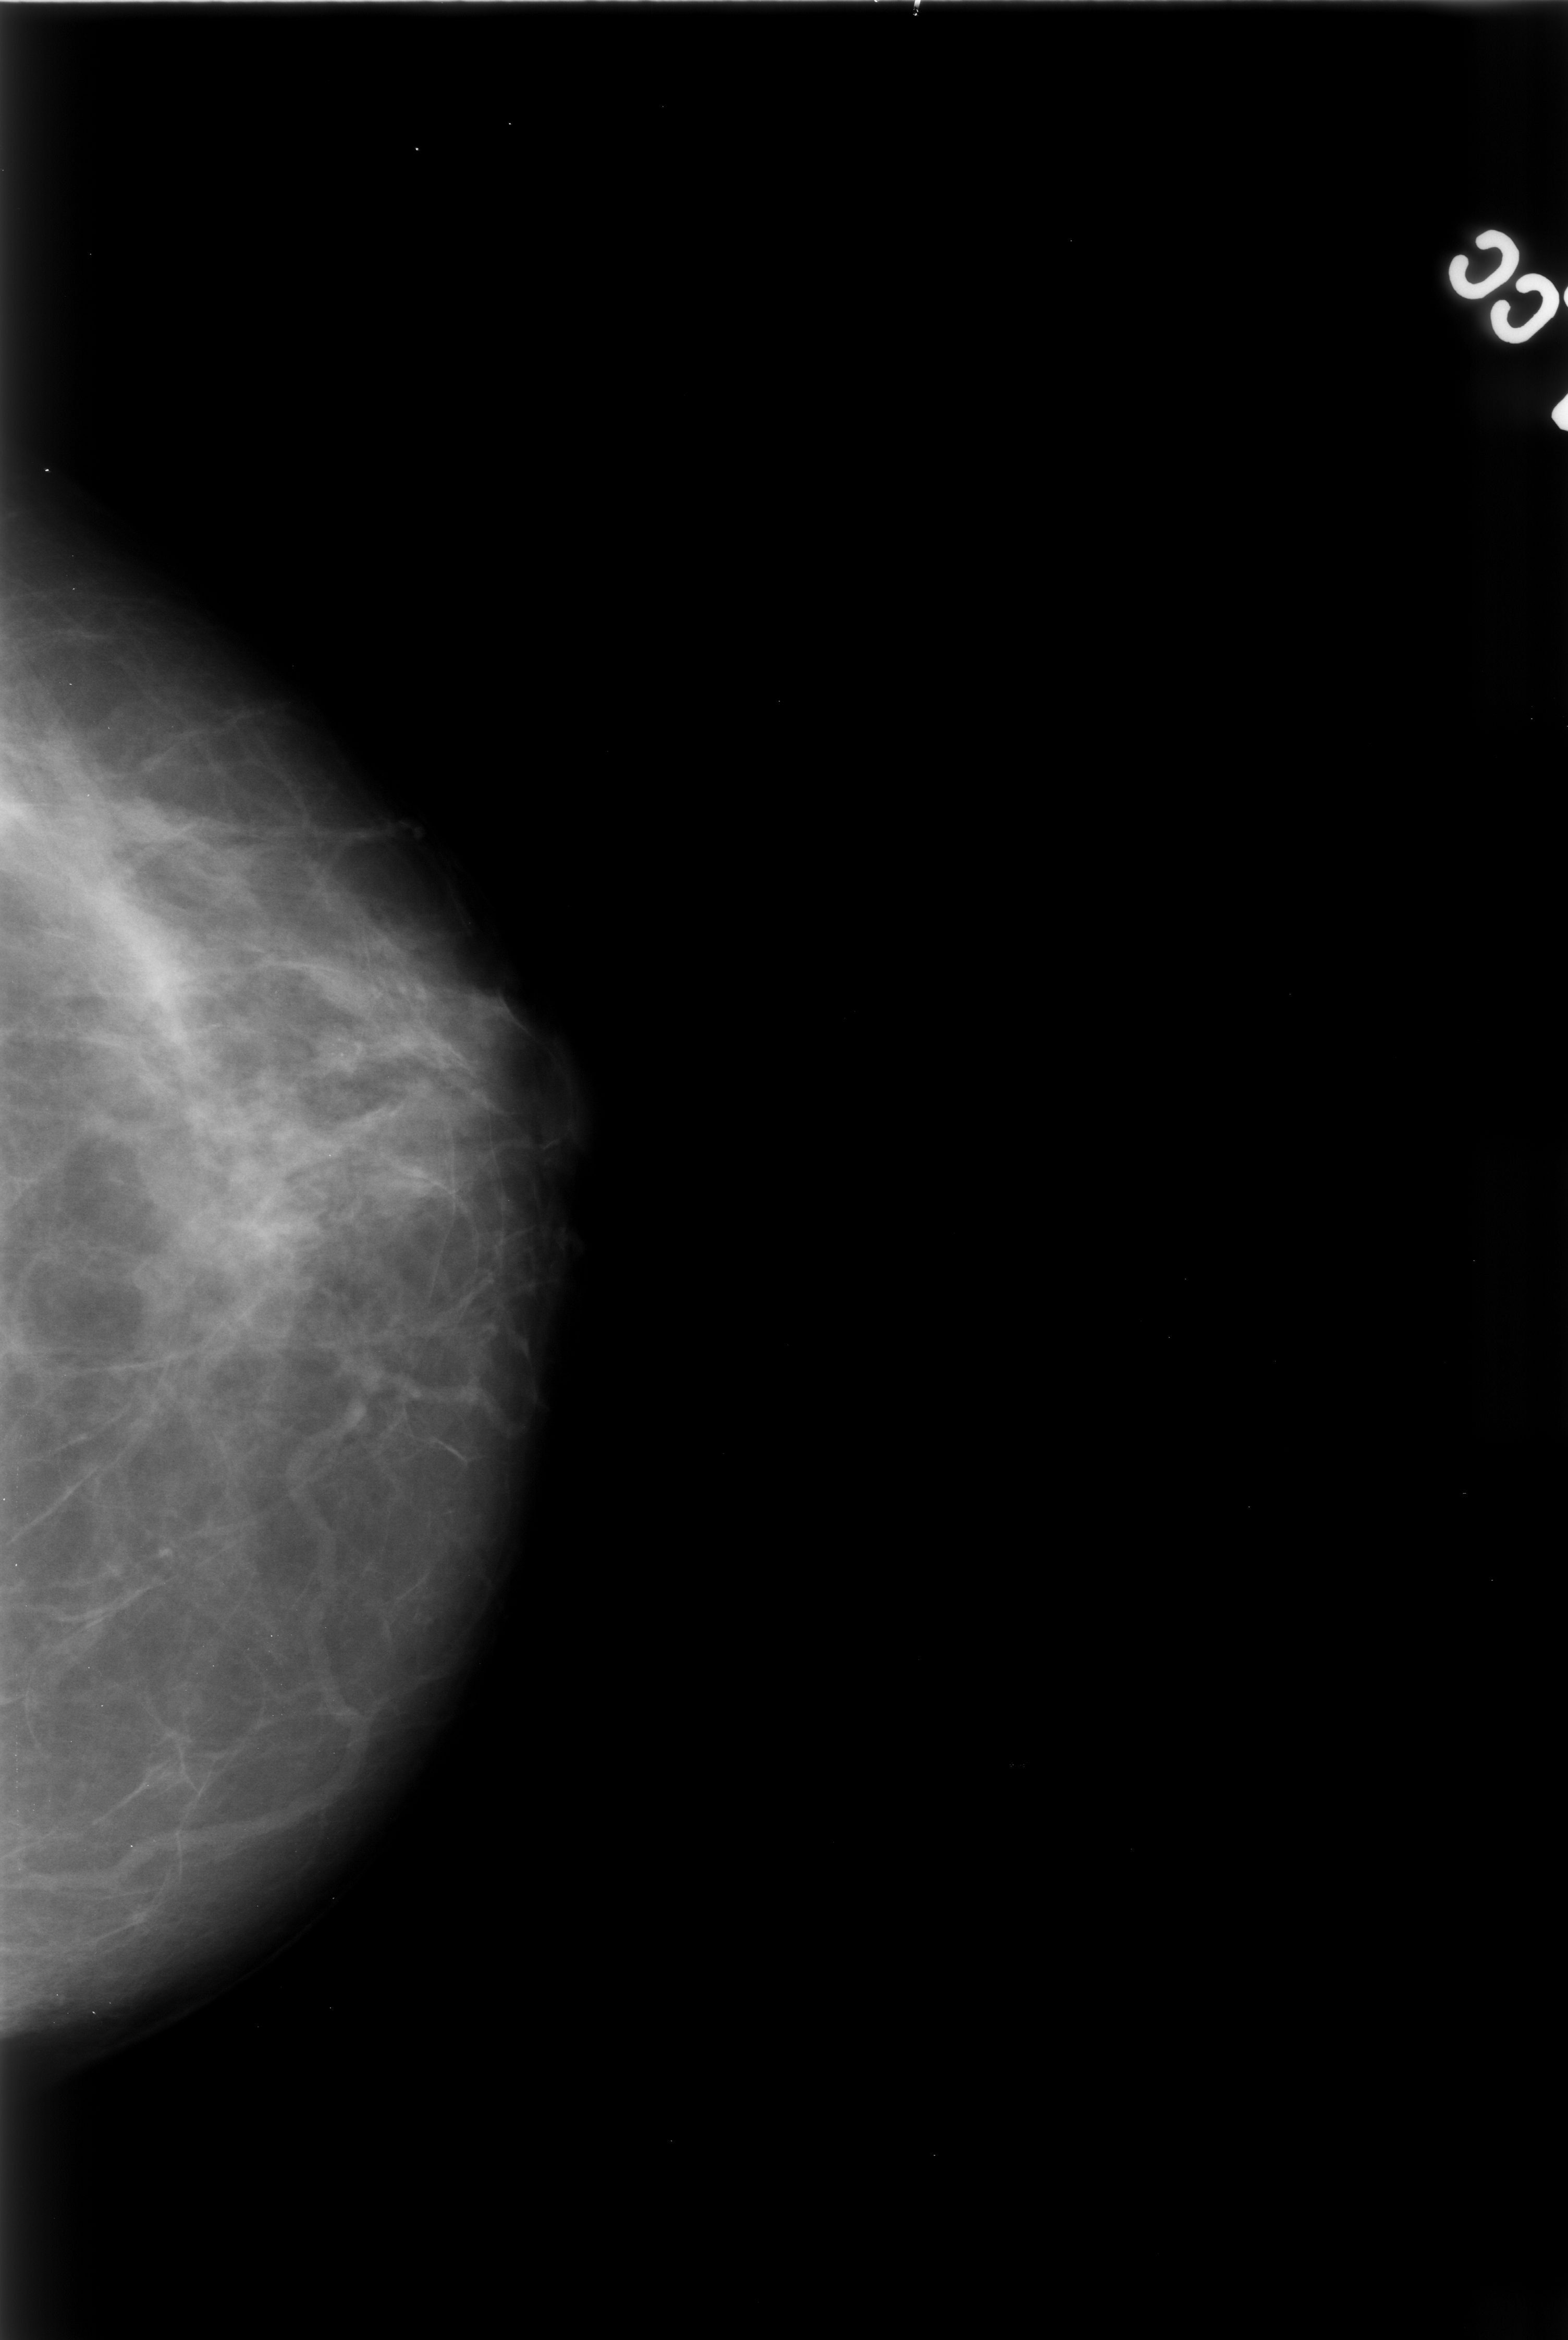
Mammogram (digitized film), left breast, craniocaudal (CC) view.
- Radiologist-marked abnormalities on this image: calcifications, morphology punctate, distribution clustered; BI-RADS assessment category 4; pathology (as recorded): benign.